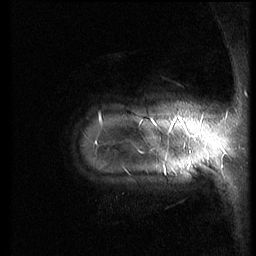
Breast MRI (dynamic contrast-enhanced), one sagittal slice; slice 12 of 66 in the series (ordered by position); dynamic contrast-enhanced series, image 2 of 3 at this slice position (ordered by acquisition); 1.5 T; TE 4.2 ms, TR 8.9 ms; 2.5 mm slice thickness; 256 × 256 image matrix. Patient: female, 39 years. Case-level facts recorded for this patient, not image findings: setting: breast cancer imaged before/during neoadjuvant chemotherapy; receptor status: HER2-positive.
Annotated regions visible in this slice (semi-automatically segmented with operator editing):
- analysis volume of interest (the breast-tissue region the enhancement analysis was run in; not a lesion): bounding box (x1, y1, x2, y2) in pixels: (64, 75, 188, 216)
- tumour enhancement mask (voxels above the 140 % enhancement threshold inside the analysis volume of interest): (170, 127, 172, 130)